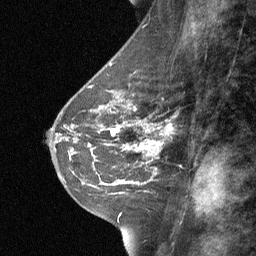
Breast MRI (dynamic contrast-enhanced), one sagittal slice. Slice 30 of 64 in the series (ordered by position). Dynamic contrast-enhanced study with each time point stored as its own series, time point 2 of 3 at this slice position (early post-contrast, ordered by acquisition time). 1.5 T. TE 4.8 ms, TR 27 ms. 2 mm slice thickness. 256 × 256 image matrix. Female patient, age 42 years. Case-level facts recorded for this patient, not image findings: setting: breast cancer imaged before/during neoadjuvant chemotherapy; receptor status: triple-negative.
Outlined on this slice (semi-automatically segmented with operator editing):
- analysis volume of interest (the breast-tissue region the enhancement analysis was run in; not a lesion): bounding box [x1, y1, x2, y2] px = [99, 117, 174, 187]
- tumour enhancement mask (voxels above the 90 % enhancement threshold inside the analysis volume of interest): [121, 121, 170, 184]